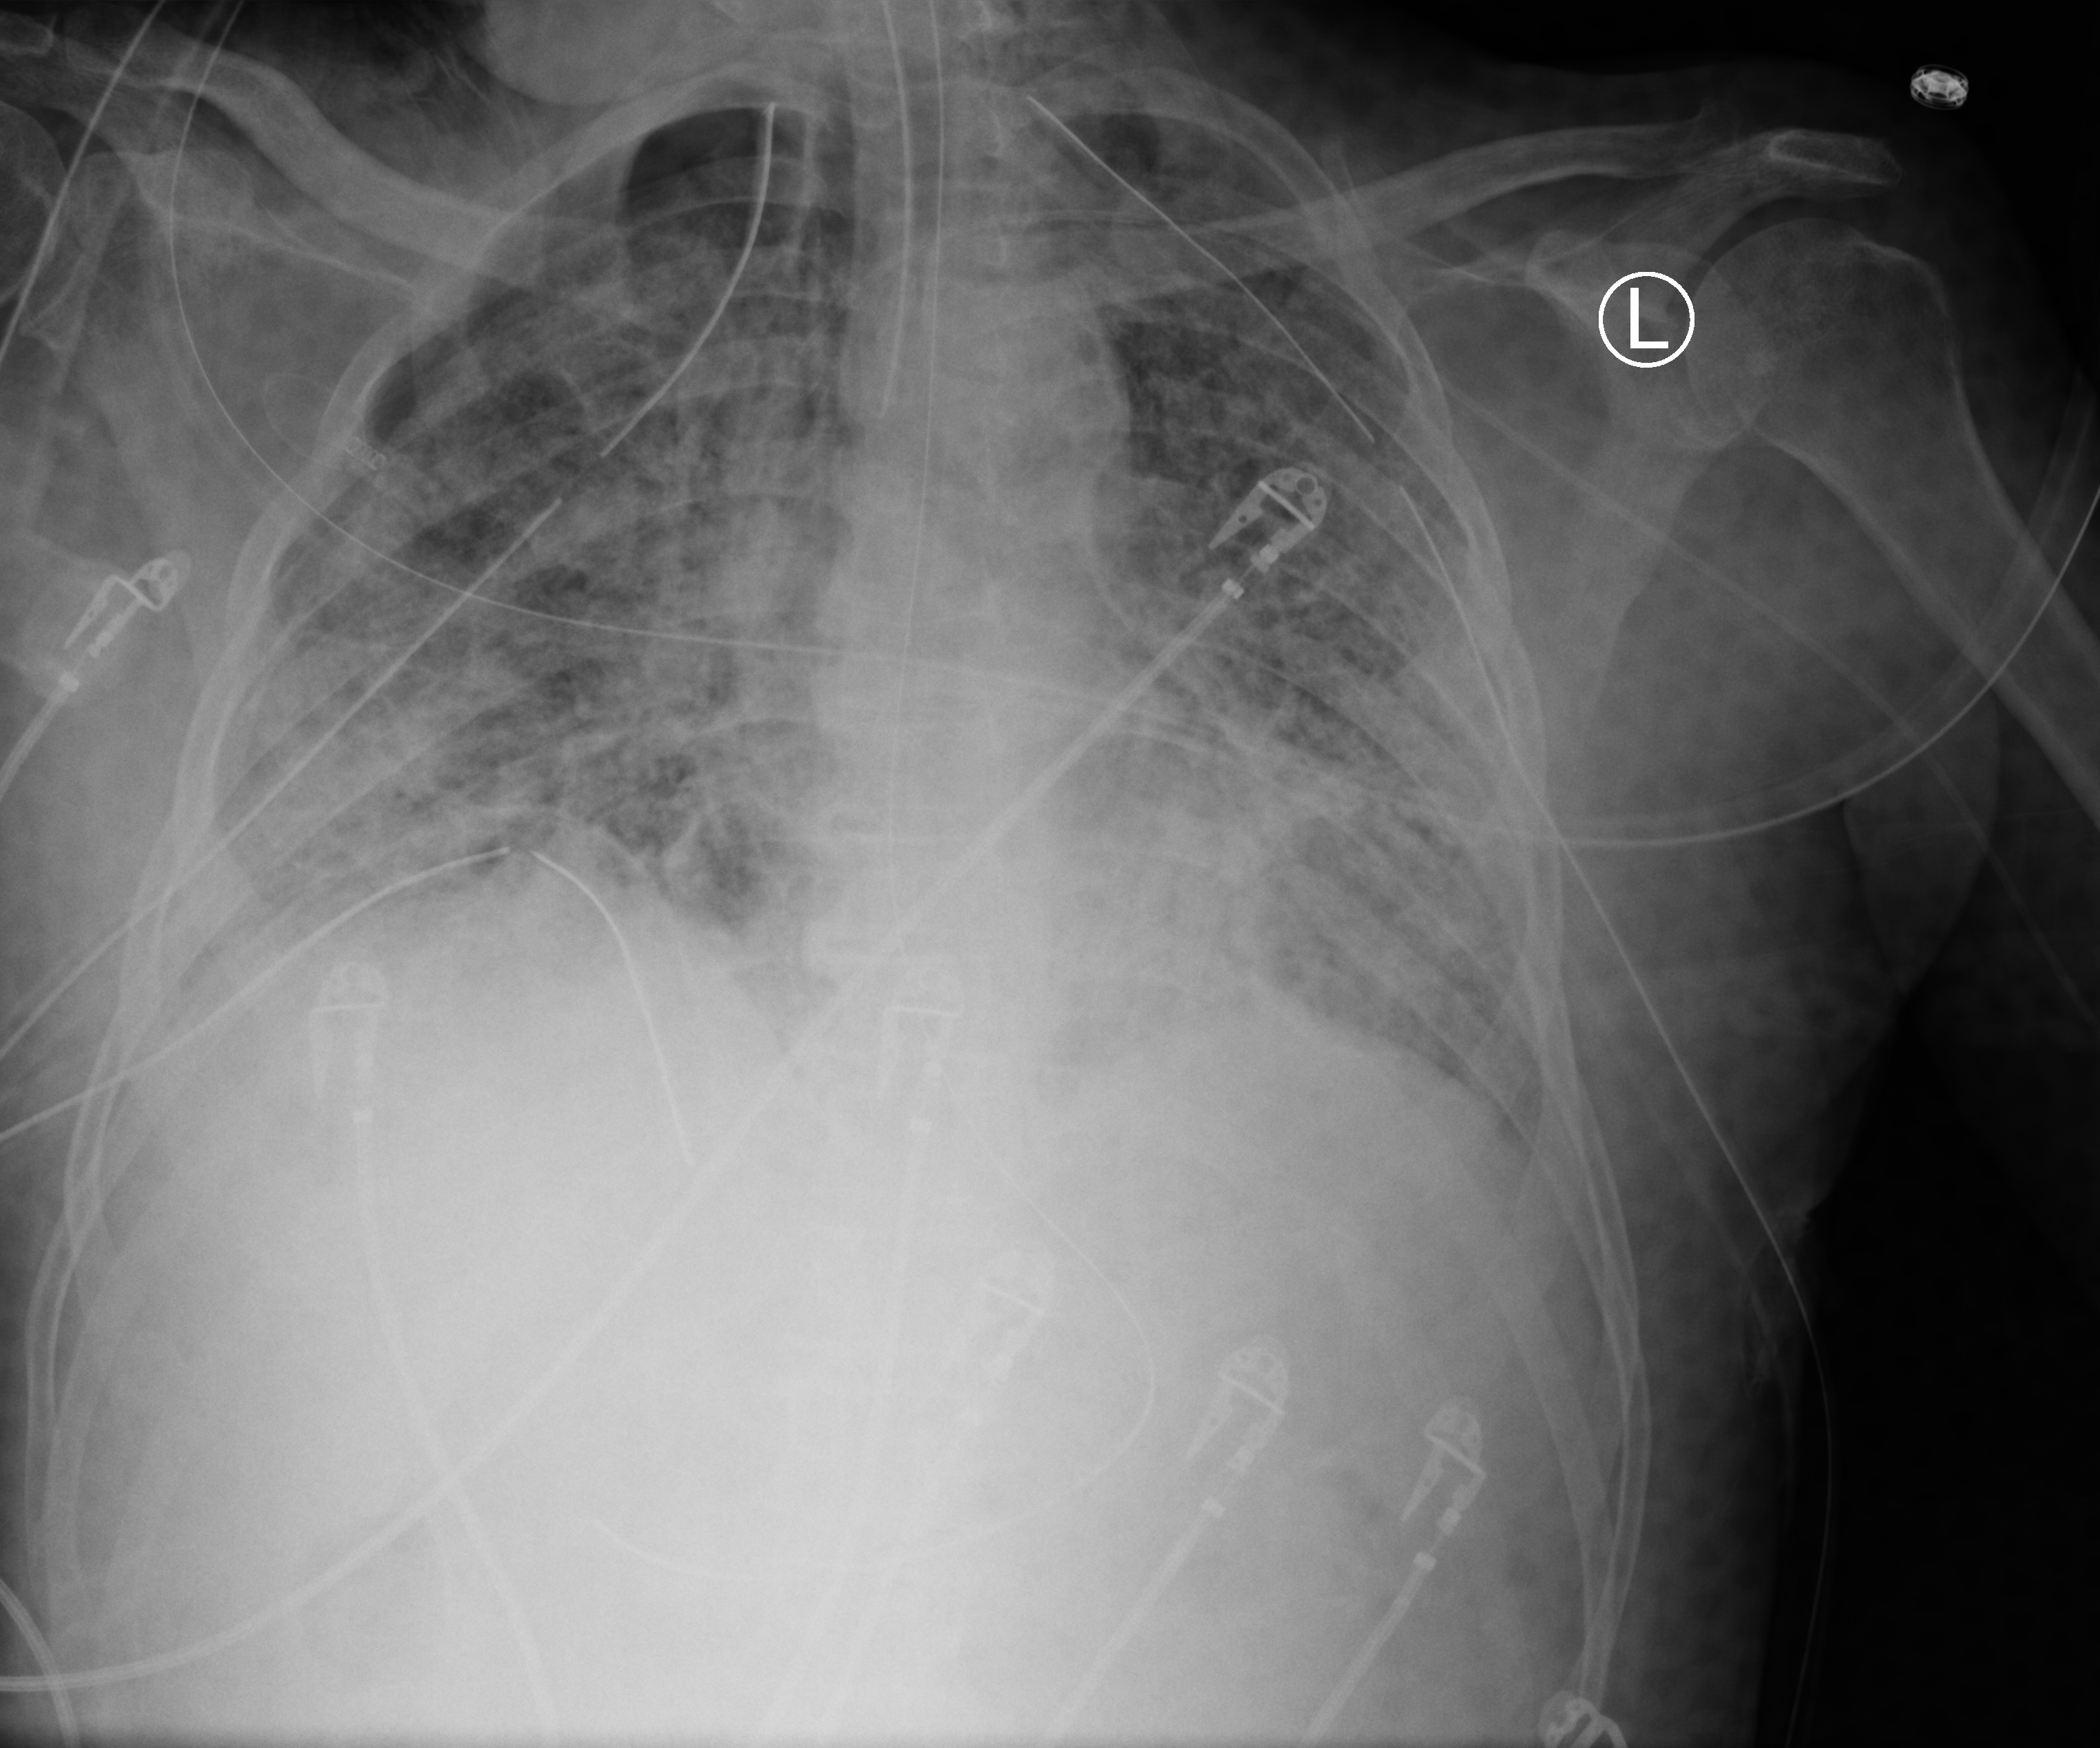
Portable chest radiograph, anteroposterior (AP) projection. Patient hospitalised with COVID-19; male, aged 18–59 years.
From the hospital-stay record, not from the radiograph (when in the stay this image was taken is not recorded):
- admitted to intensive care during this hospital stay: yes